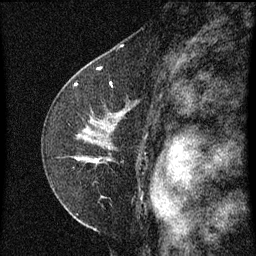
Breast MRI (dynamic contrast-enhanced), one sagittal slice. Position 44 of 60 along the scan axis. Dynamic contrast-enhanced series, image 2 of 3 at this slice position (ordered by acquisition). 1.5 T. TE 4.2 ms, TR 8 ms. 2 mm slice thickness. 256 × 256 image matrix. Patient: female, 47 years.
Outlined on this slice (semi-automatically segmented with operator editing):
- analysis volume of interest (the breast-tissue region the enhancement analysis was run in; not a lesion): bounding box [x1, y1, x2, y2] px = [50, 84, 141, 199]
- tumour enhancement mask (voxels above the 70 % enhancement threshold inside the analysis volume of interest): [76, 84, 99, 163]